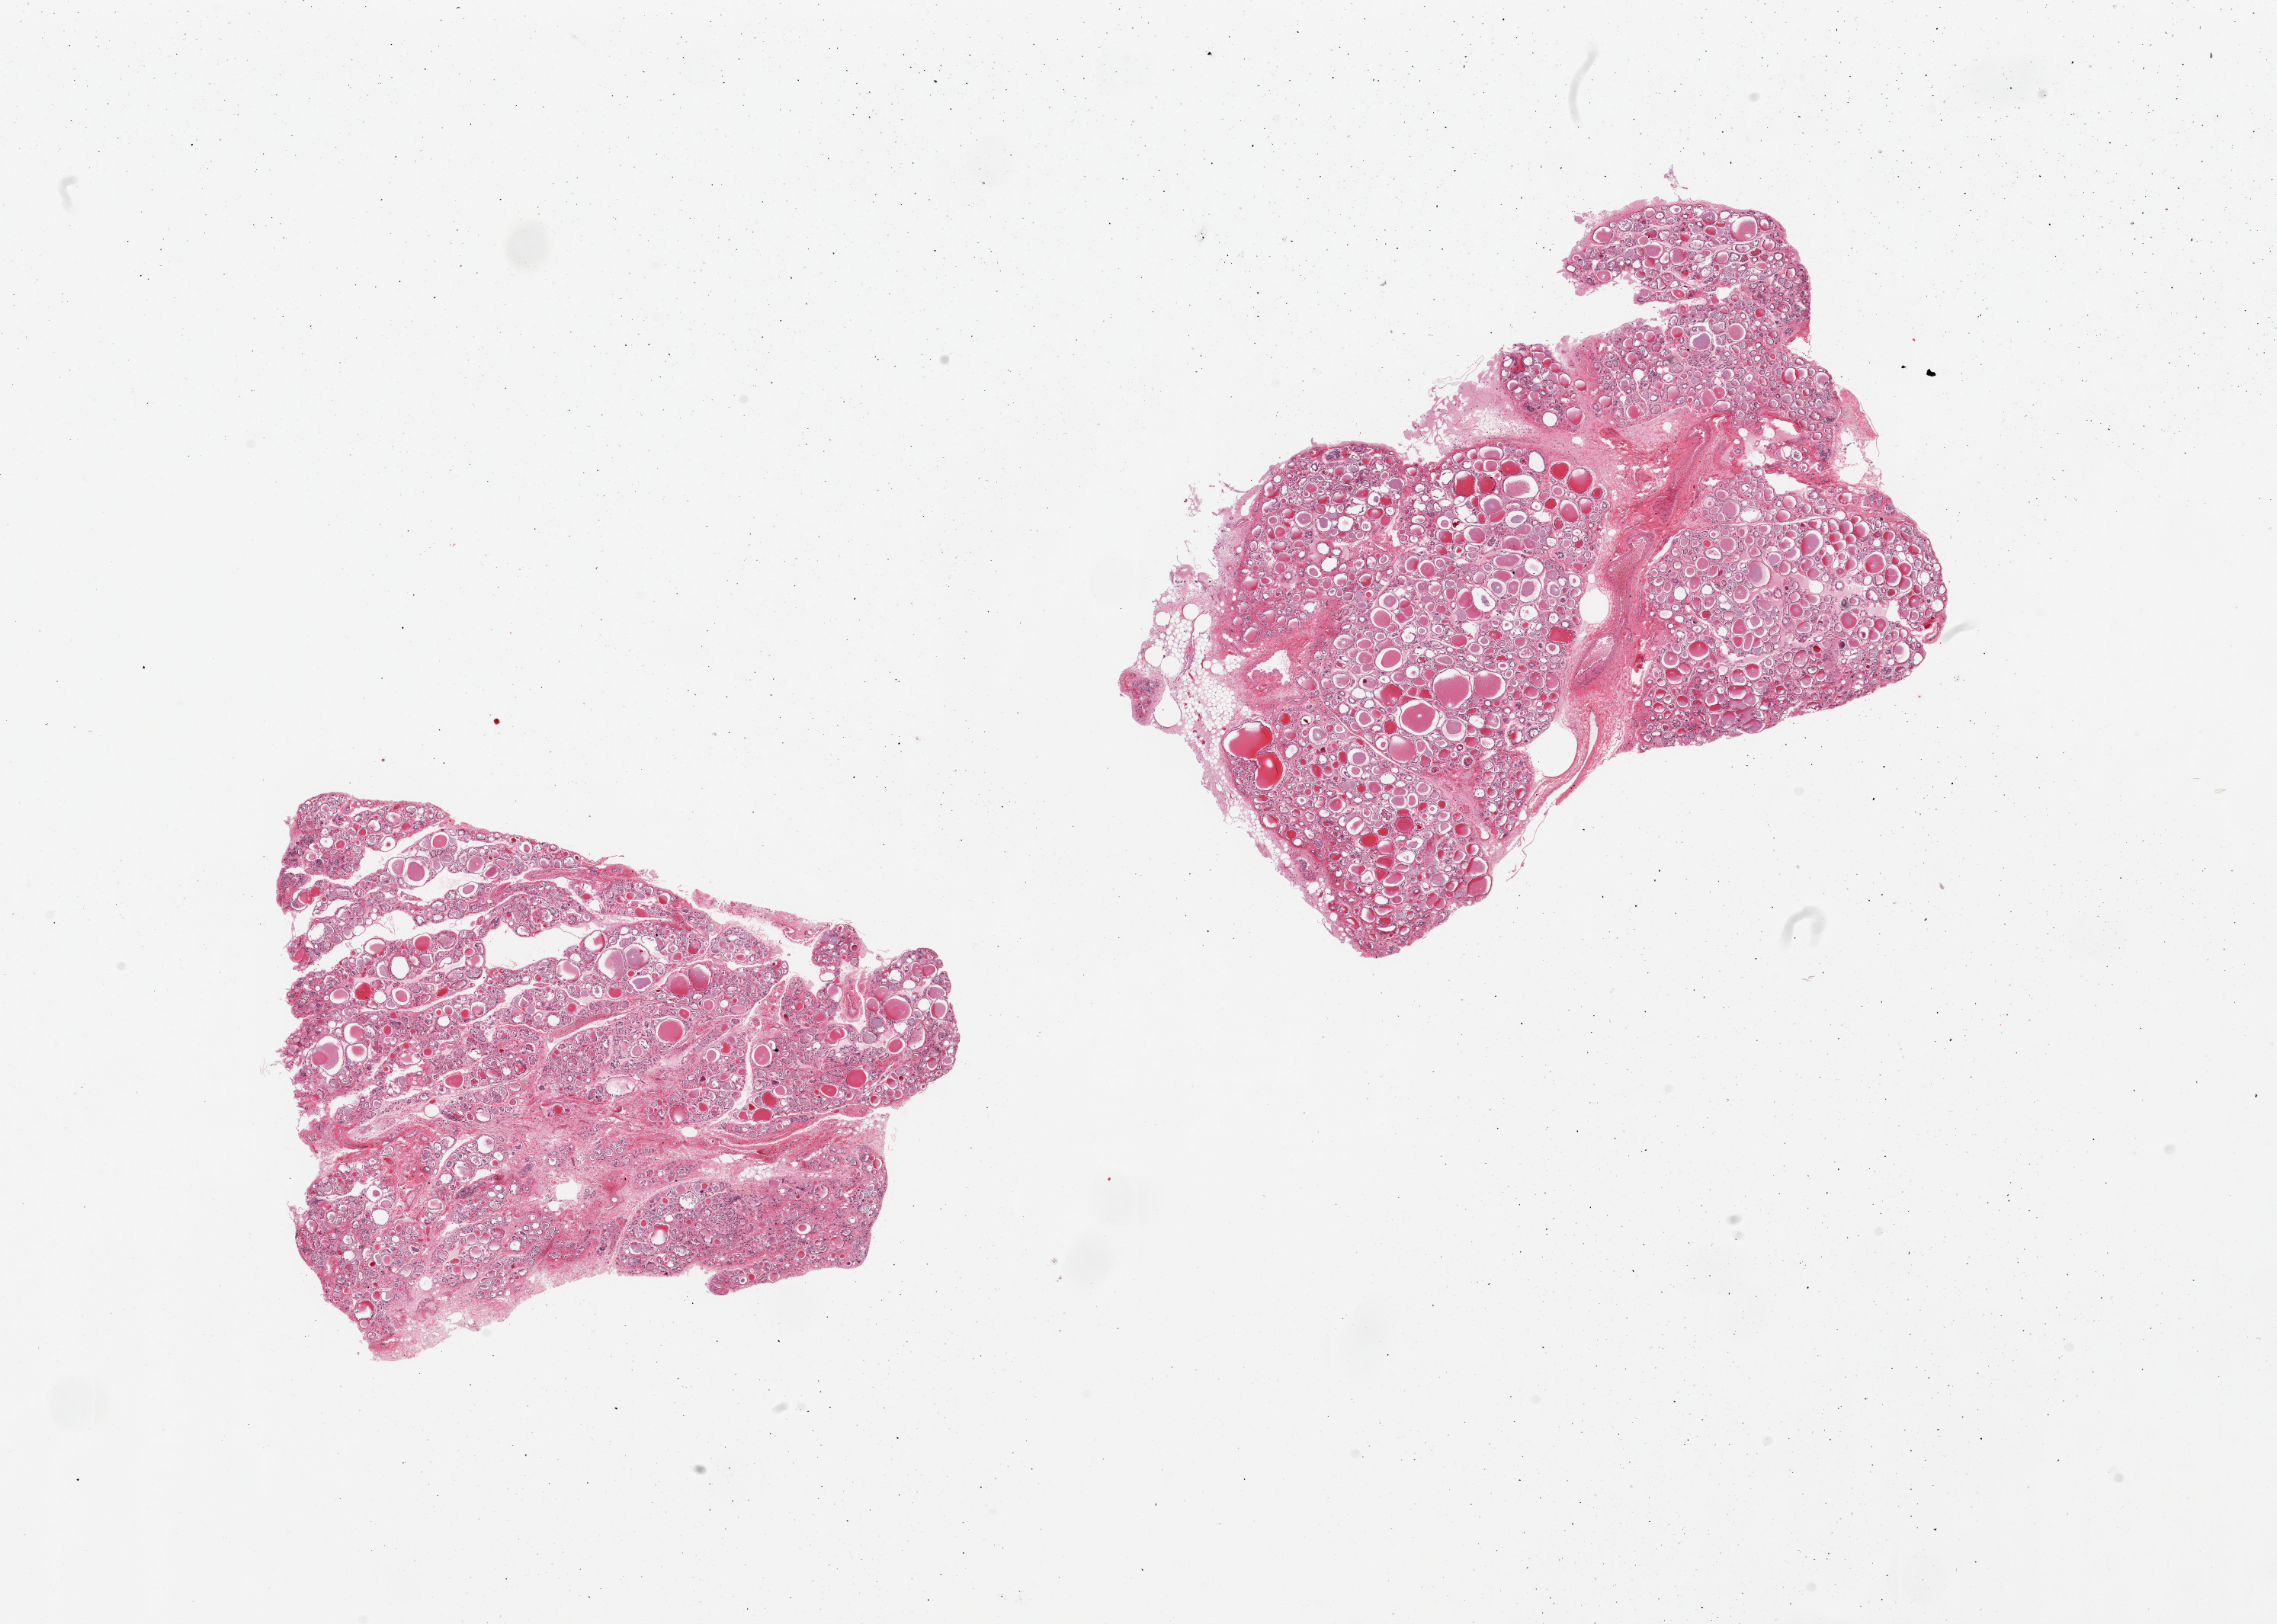
Digitized hematoxylin and eosin (H&E)-stained section — whole scanned area (about 23.6 x 16.9 mm) shown as a low-resolution overview; PAXgene-fixed paraffin-embedded (PFPE) section; section of thyroid (target tissue); tissue donor sample. Donor: female.
Pathologist's review note for this sample: 2 pieces.